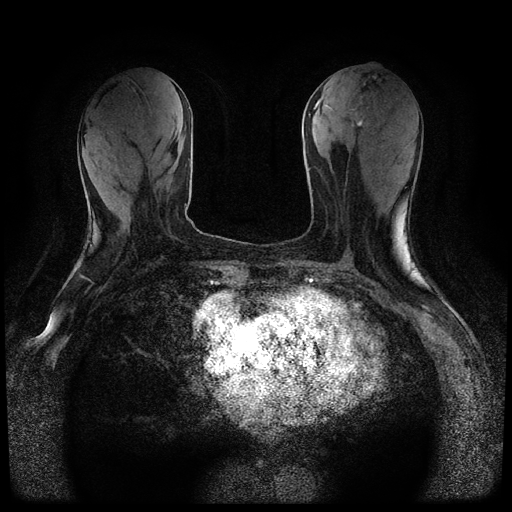
Breast MRI (dynamic contrast-enhanced, multi-phase), one axial slice. Slice 27 of 116 in the series (ordered by position). Dynamic contrast-enhanced series, time point 2 of 5 at this slice position (early post-contrast). 1.5 T. TE 2.7 ms, TR 5.4 ms. 512 × 512 image matrix. Female patient, age 80 years.
Annotated regions visible in this slice (semi-automatically segmented with operator editing):
- breast lesion (labelled 'tumour' in the annotation; benign lesions carry a separate 'benign' label): box from (x=352, y=117) to (x=364, y=129) px